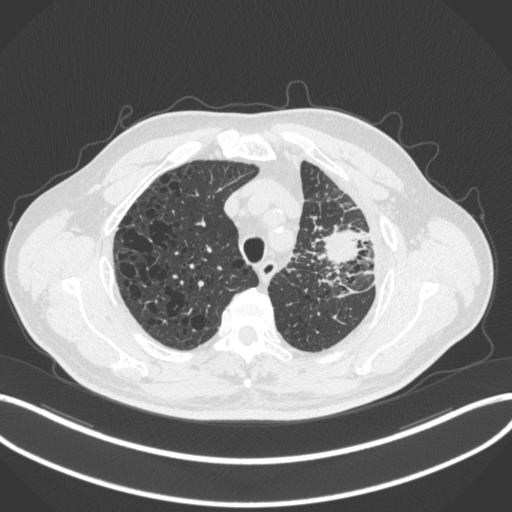
Chest CT, one axial slice; slice 243 of 286 in the series (ordered by position); 120 kVp; lung window (W 1500 / L -600 HU); 1 mm slice thickness; 512 × 512 image matrix, field of view 400 × 400 mm. Male patient, age 68 years. From the clinical record (not read from this slice): clinical TNM (as recorded): T3 N3 M1.
Outlined on this slice (bounding box drawn by a radiologist):
- lung tumour (recorded histology: adenocarcinoma): box from (x=316, y=225) to (x=361, y=268) px